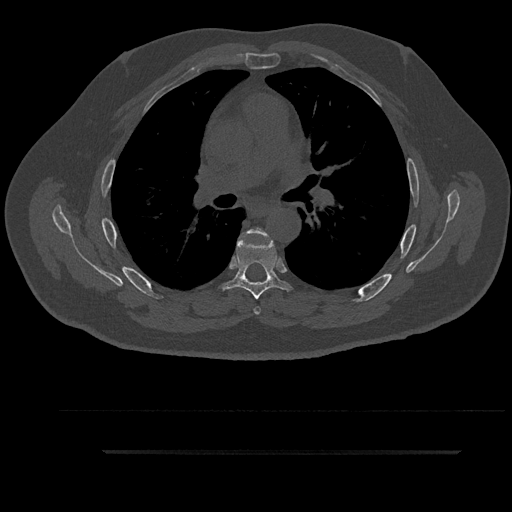
CT including the spine, one axial slice. Slice 587 of 797 in the series (ordered by position). Reconstruction kernel Br40s/3. Bone window (W 1800 / L 400 HU). 0.5 mm slice thickness. 512 × 512 image matrix, field of view 432 × 432 mm. Male patient, age 63 years. Case-level facts recorded for this patient, not image findings: primary cancer: renal.
Structures marked on this image (semi-automatically segmented with operator editing):
- T5 vertebra: box from (x=242, y=227) to (x=268, y=315) px
- T6 vertebra: (x=222, y=233)–(x=290, y=300)